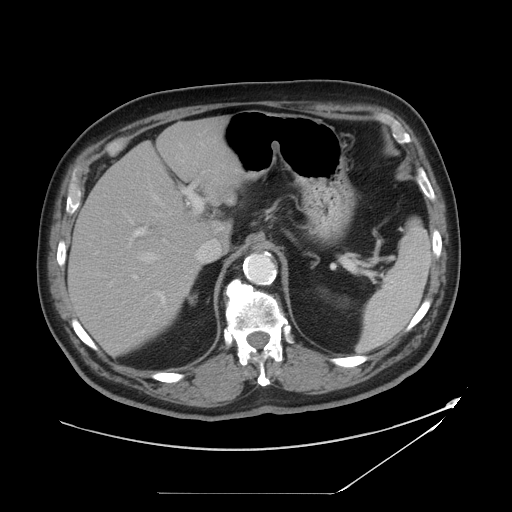
Contrast-enhanced abdominal CT, one axial slice. Slice 31 of 49 in the series (ordered by position). Reconstruction kernel STANDARD. Intravenous contrast given. Soft-tissue window (W 400 / L 40 HU). 512 × 512 image matrix. Male patient, age 72 years. Case-level facts recorded for this patient, not image findings: diagnosis: colorectal cancer liver metastases, imaged before liver resection; multiple liver metastases: no; largest metastasis: 2.5 cm; chemotherapy before resection: yes.
Structures marked on this image (manually delineated by an expert):
- hepatic veins: bounding box [x1, y1, x2, y2] px = [130, 184, 171, 272]
- liver: [69, 120, 238, 354]
- planned liver remnant (the part of the liver to remain after resection): [69, 169, 199, 354]
- portal vein (with intrahepatic branches): [111, 171, 205, 304]
- liver metastasis: [211, 182, 229, 199]